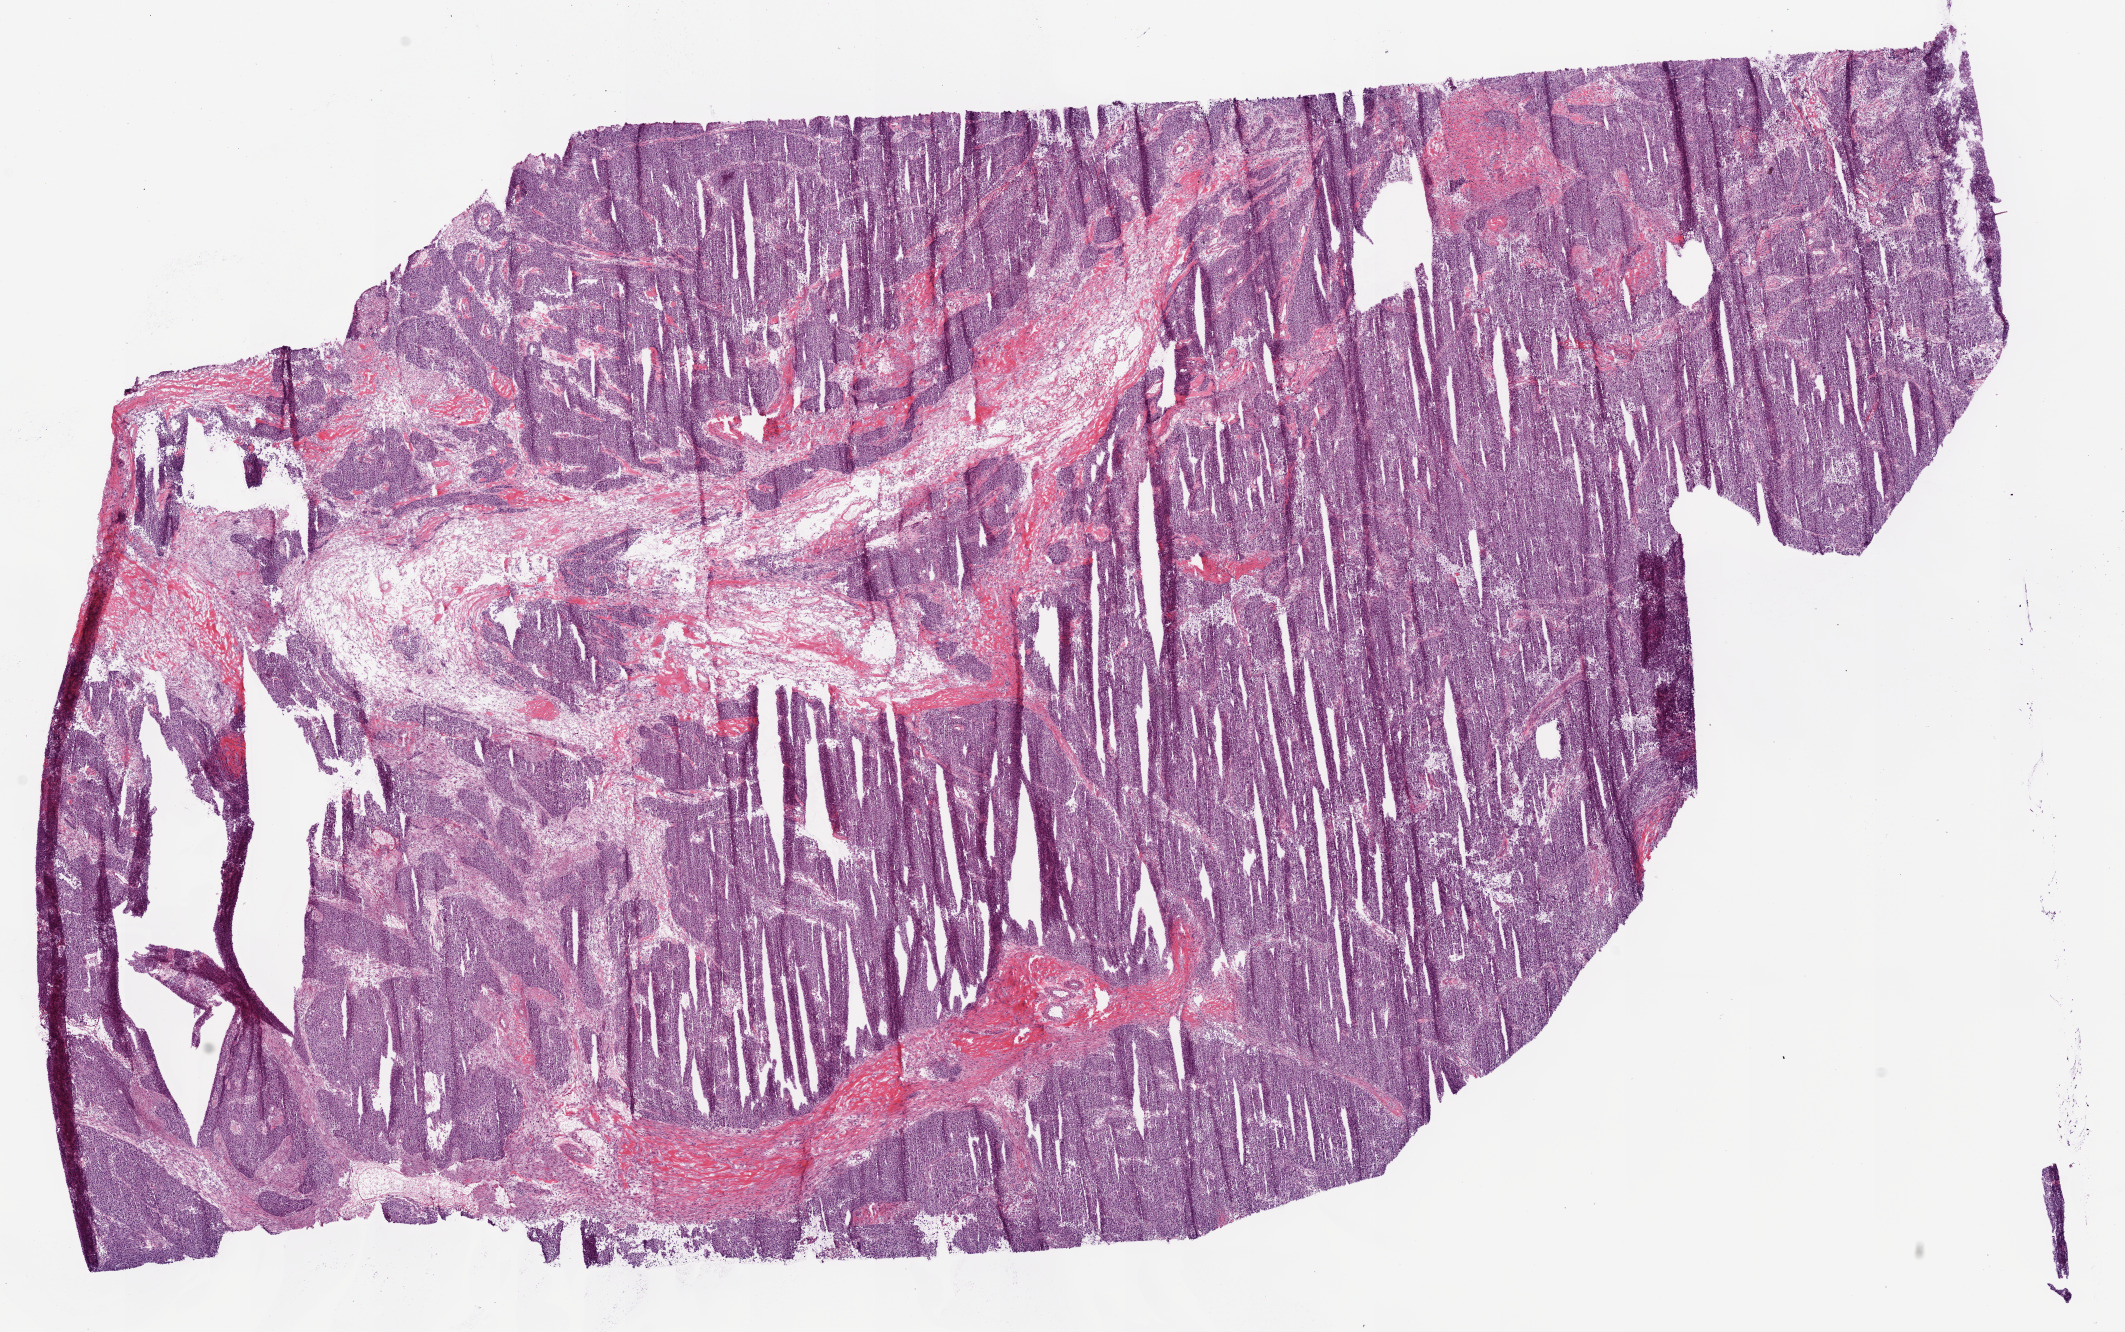
Digitized Hematoxylin and eosin (H&E) stained tissue section (whole slide) — shown as a low-resolution overview of the whole scanned area (about 17.1 x 10.7 mm); frozen section from the bottom of the tissue portion; sample: primary tumour, ovary. Female, age 42 years at initial diagnosis. Histologic grade: G3 (poorly differentiated). Pathologist review of this section (percent, as recorded): tumour cells 72%, tumour nuclei 85%, normal cells 0%, stromal cells 18%, necrosis 10%.
Diagnosis: Serous cystadenocarcinoma, NOS. FIGO stage: IIIA. Laterality: bilateral.